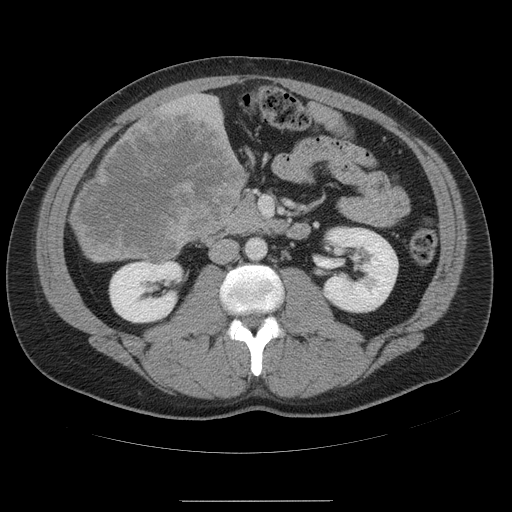
Contrast-enhanced abdominal CT, one axial slice. Position 17 of 54 along the scan axis. 120 kVp. Intravenous contrast given. Soft-tissue window (W 400 / L 40 HU). 5 mm slice thickness. 512 × 512 image matrix, field of view 436 × 436 mm. Male patient, age 40 years. From the clinical record (not read from this slice): diagnosis: colorectal cancer liver metastases, imaged before liver resection; multiple liver metastases: no; largest metastasis: 15 cm; disease in both lobes: no.
Structures marked on this image (expert manual segmentation):
- liver: box from (x=72, y=94) to (x=245, y=264) px
- liver metastasis: (x=72, y=109)–(x=246, y=260)